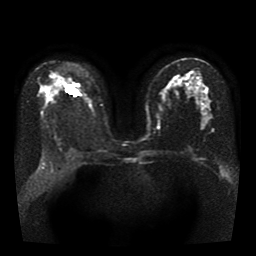
Breast MRI, one axial slice. Position 24 of 41 along the scan axis. Diffusion-weighted series; image 2 of 4 stored at this slice position (different b-values; order by instance number). 1.5 T. 256 × 256 image matrix, field of view 330 × 330 mm. Female patient.
Annotated regions visible in this slice (manually delineated by an expert):
- tumour on diffusion-weighted imaging: bounding box (x1, y1, x2, y2) in pixels: (67, 86, 79, 96)